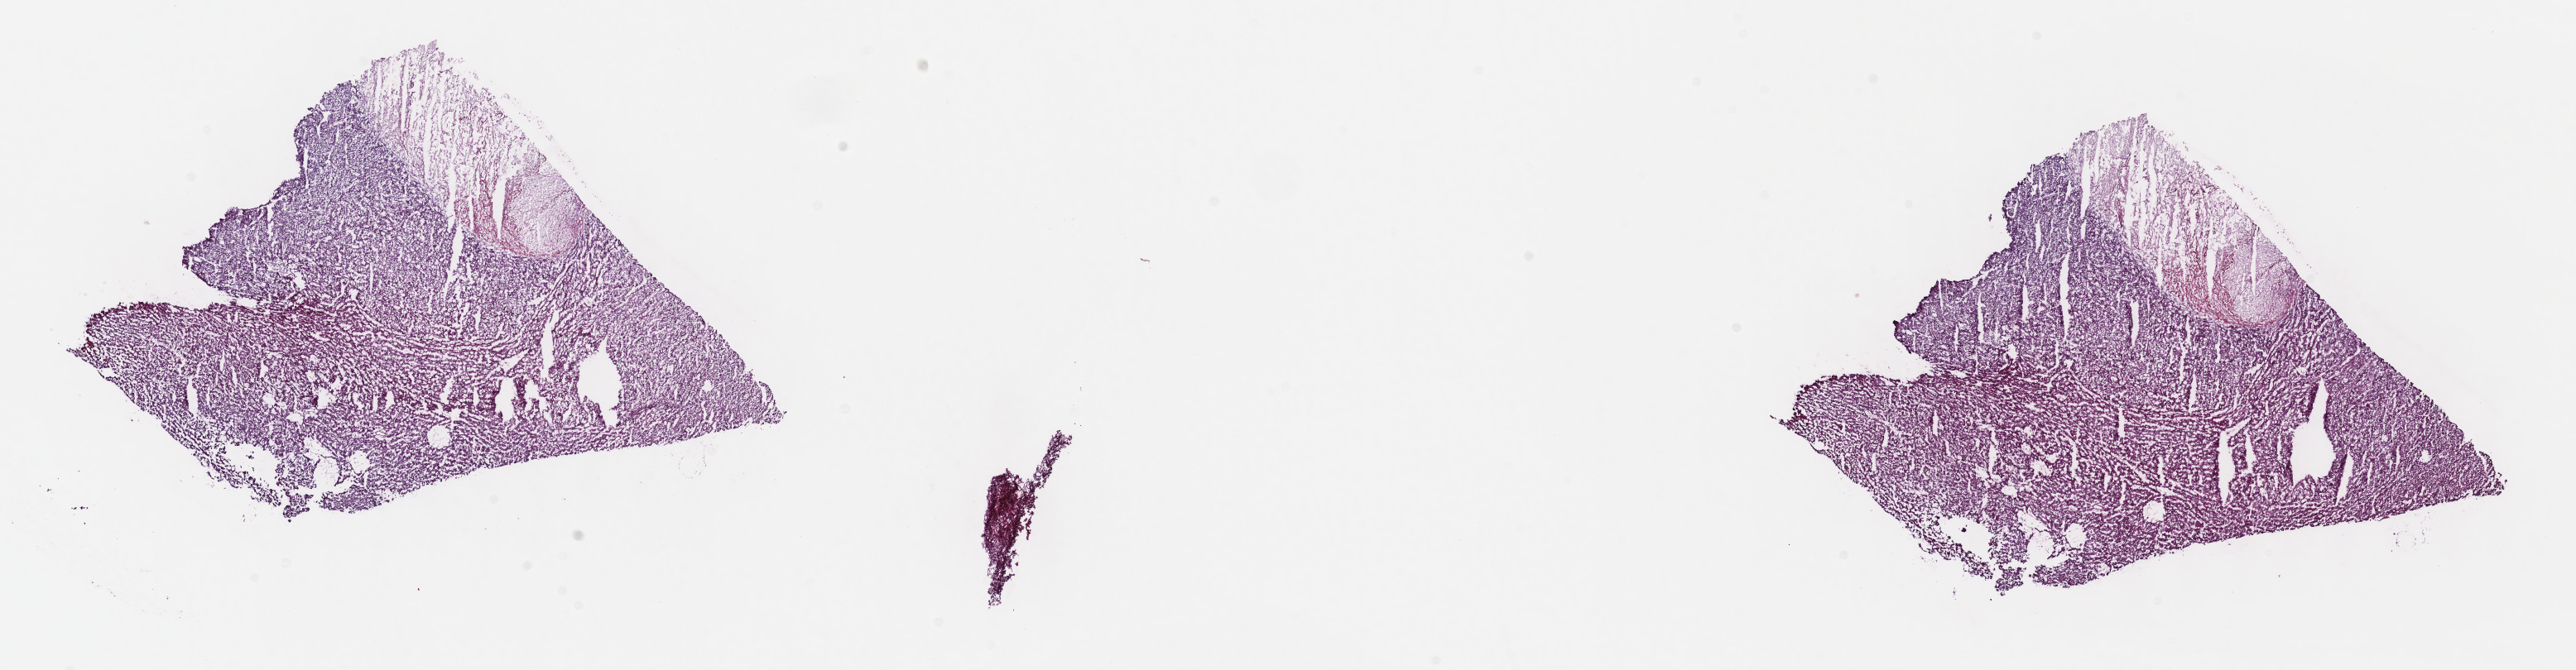
Digitized H&E tissue section (whole slide) — whole scanned area (about 25.2 x 6.6 mm, from a 40x scan) shown as a low-resolution overview, frozen section from the top of the tissue portion, sample: primary tumour, liver. Male patient; age at initial diagnosis 53 years. Pathologist review of this section (percent, as recorded): tumour cells 100%, tumour nuclei 80%.
Diagnosis: Hepatocellular carcinoma, NOS.